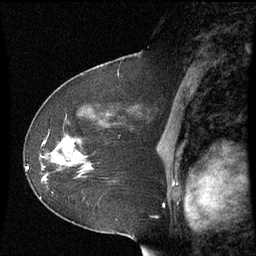
Breast MRI (dynamic contrast-enhanced), one sagittal slice; slice 35 of 60 in the series (ordered by position); dynamic contrast-enhanced series, image 2 of 3 at this slice position (ordered by acquisition); 1.5 T; TE 4.2 ms, TR 8.9 ms; 256 × 256 image matrix, field of view 210 × 210 mm. Female patient, age 51 years. Case-level facts recorded for this patient, not image findings: setting: breast cancer imaged before/during neoadjuvant chemotherapy; receptor status: HR-positive, HER2-negative.
Outlined on this slice (semi-automatically segmented with operator editing):
- analysis volume of interest (the breast-tissue region the enhancement analysis was run in; not a lesion): box from (x=50, y=117) to (x=110, y=180) px
- tumour enhancement mask (voxels above the 70 % enhancement threshold inside the analysis volume of interest): (x=63, y=139)–(x=83, y=157)